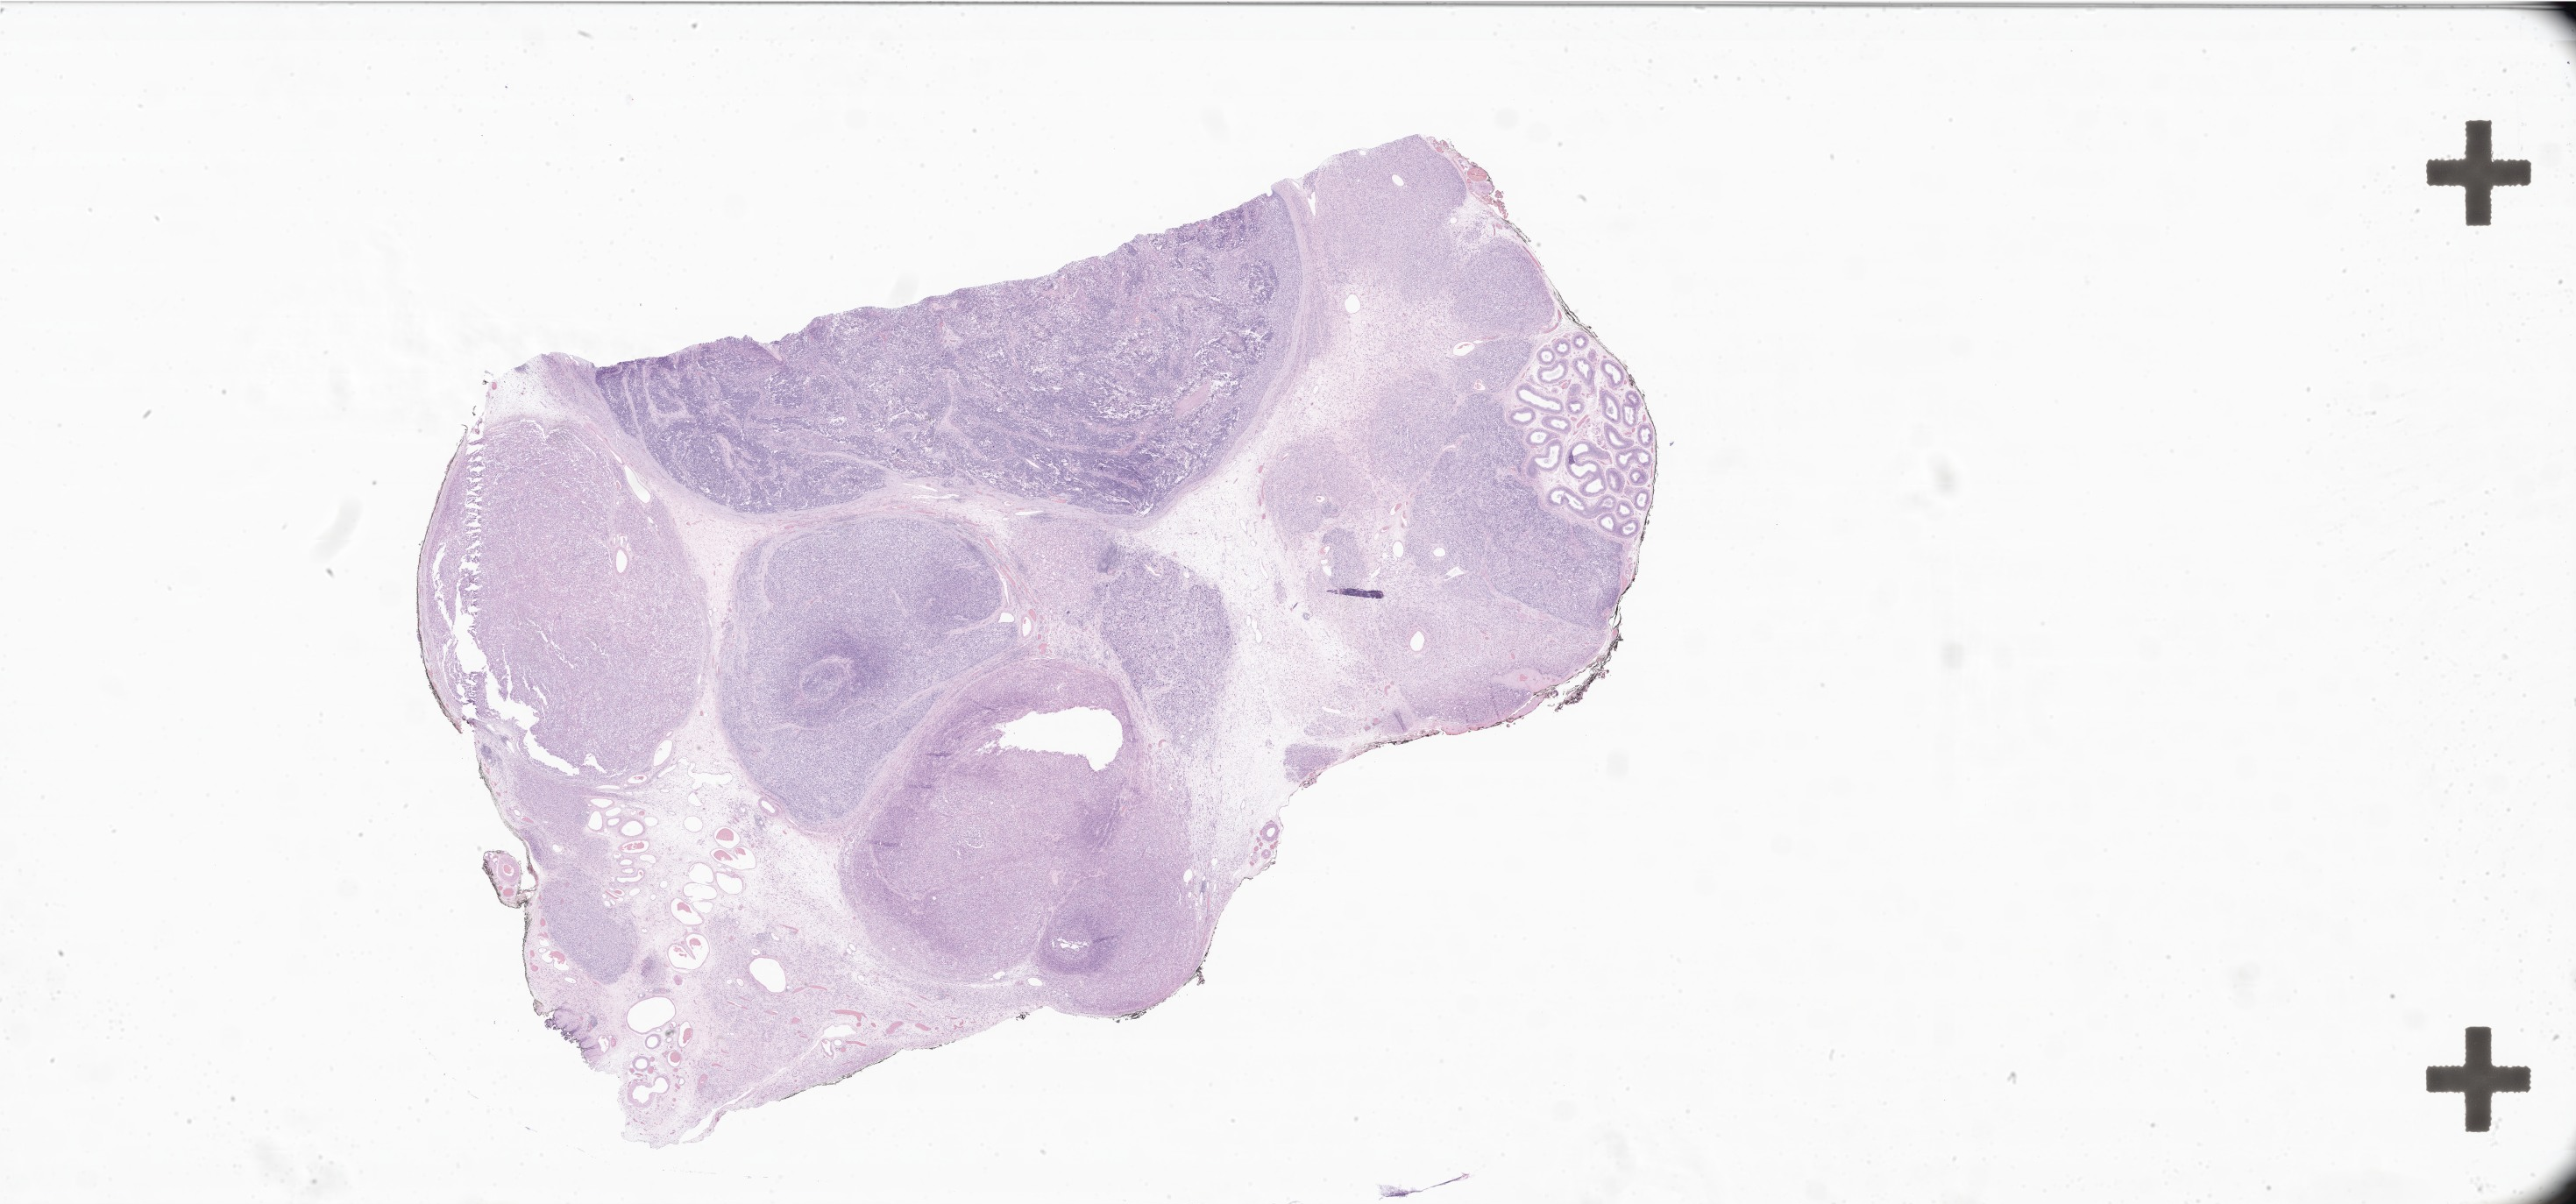
Digitized H&E-stained section of tumor tissue from the epididymis — low-resolution overview of the scanned area, about 49.6 x 23.2 mm, formalin-fixed paraffin-embedded section. Male patient, age 255 months (21 years 3 months).
Diagnosis (ICD-O-3 morphology term): Embryonal rhabdomyosarcoma, NOS.